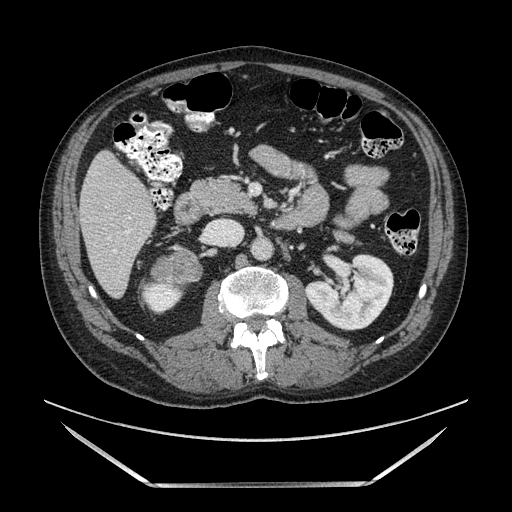
Contrast-enhanced abdominal CT, one axial slice; soft-tissue window (W 400 / L 40 HU); 1.25 mm slice thickness; 512 × 512 image matrix. Male patient. From the clinical record (not read from this slice): diagnosis: adrenocortical carcinoma; tumour side: right adrenal; tumour size at pathology: 10.3 cm.
Annotated regions visible in this slice (semi-automatically segmented with operator editing):
- mass: box from (x=151, y=245) to (x=202, y=283) px